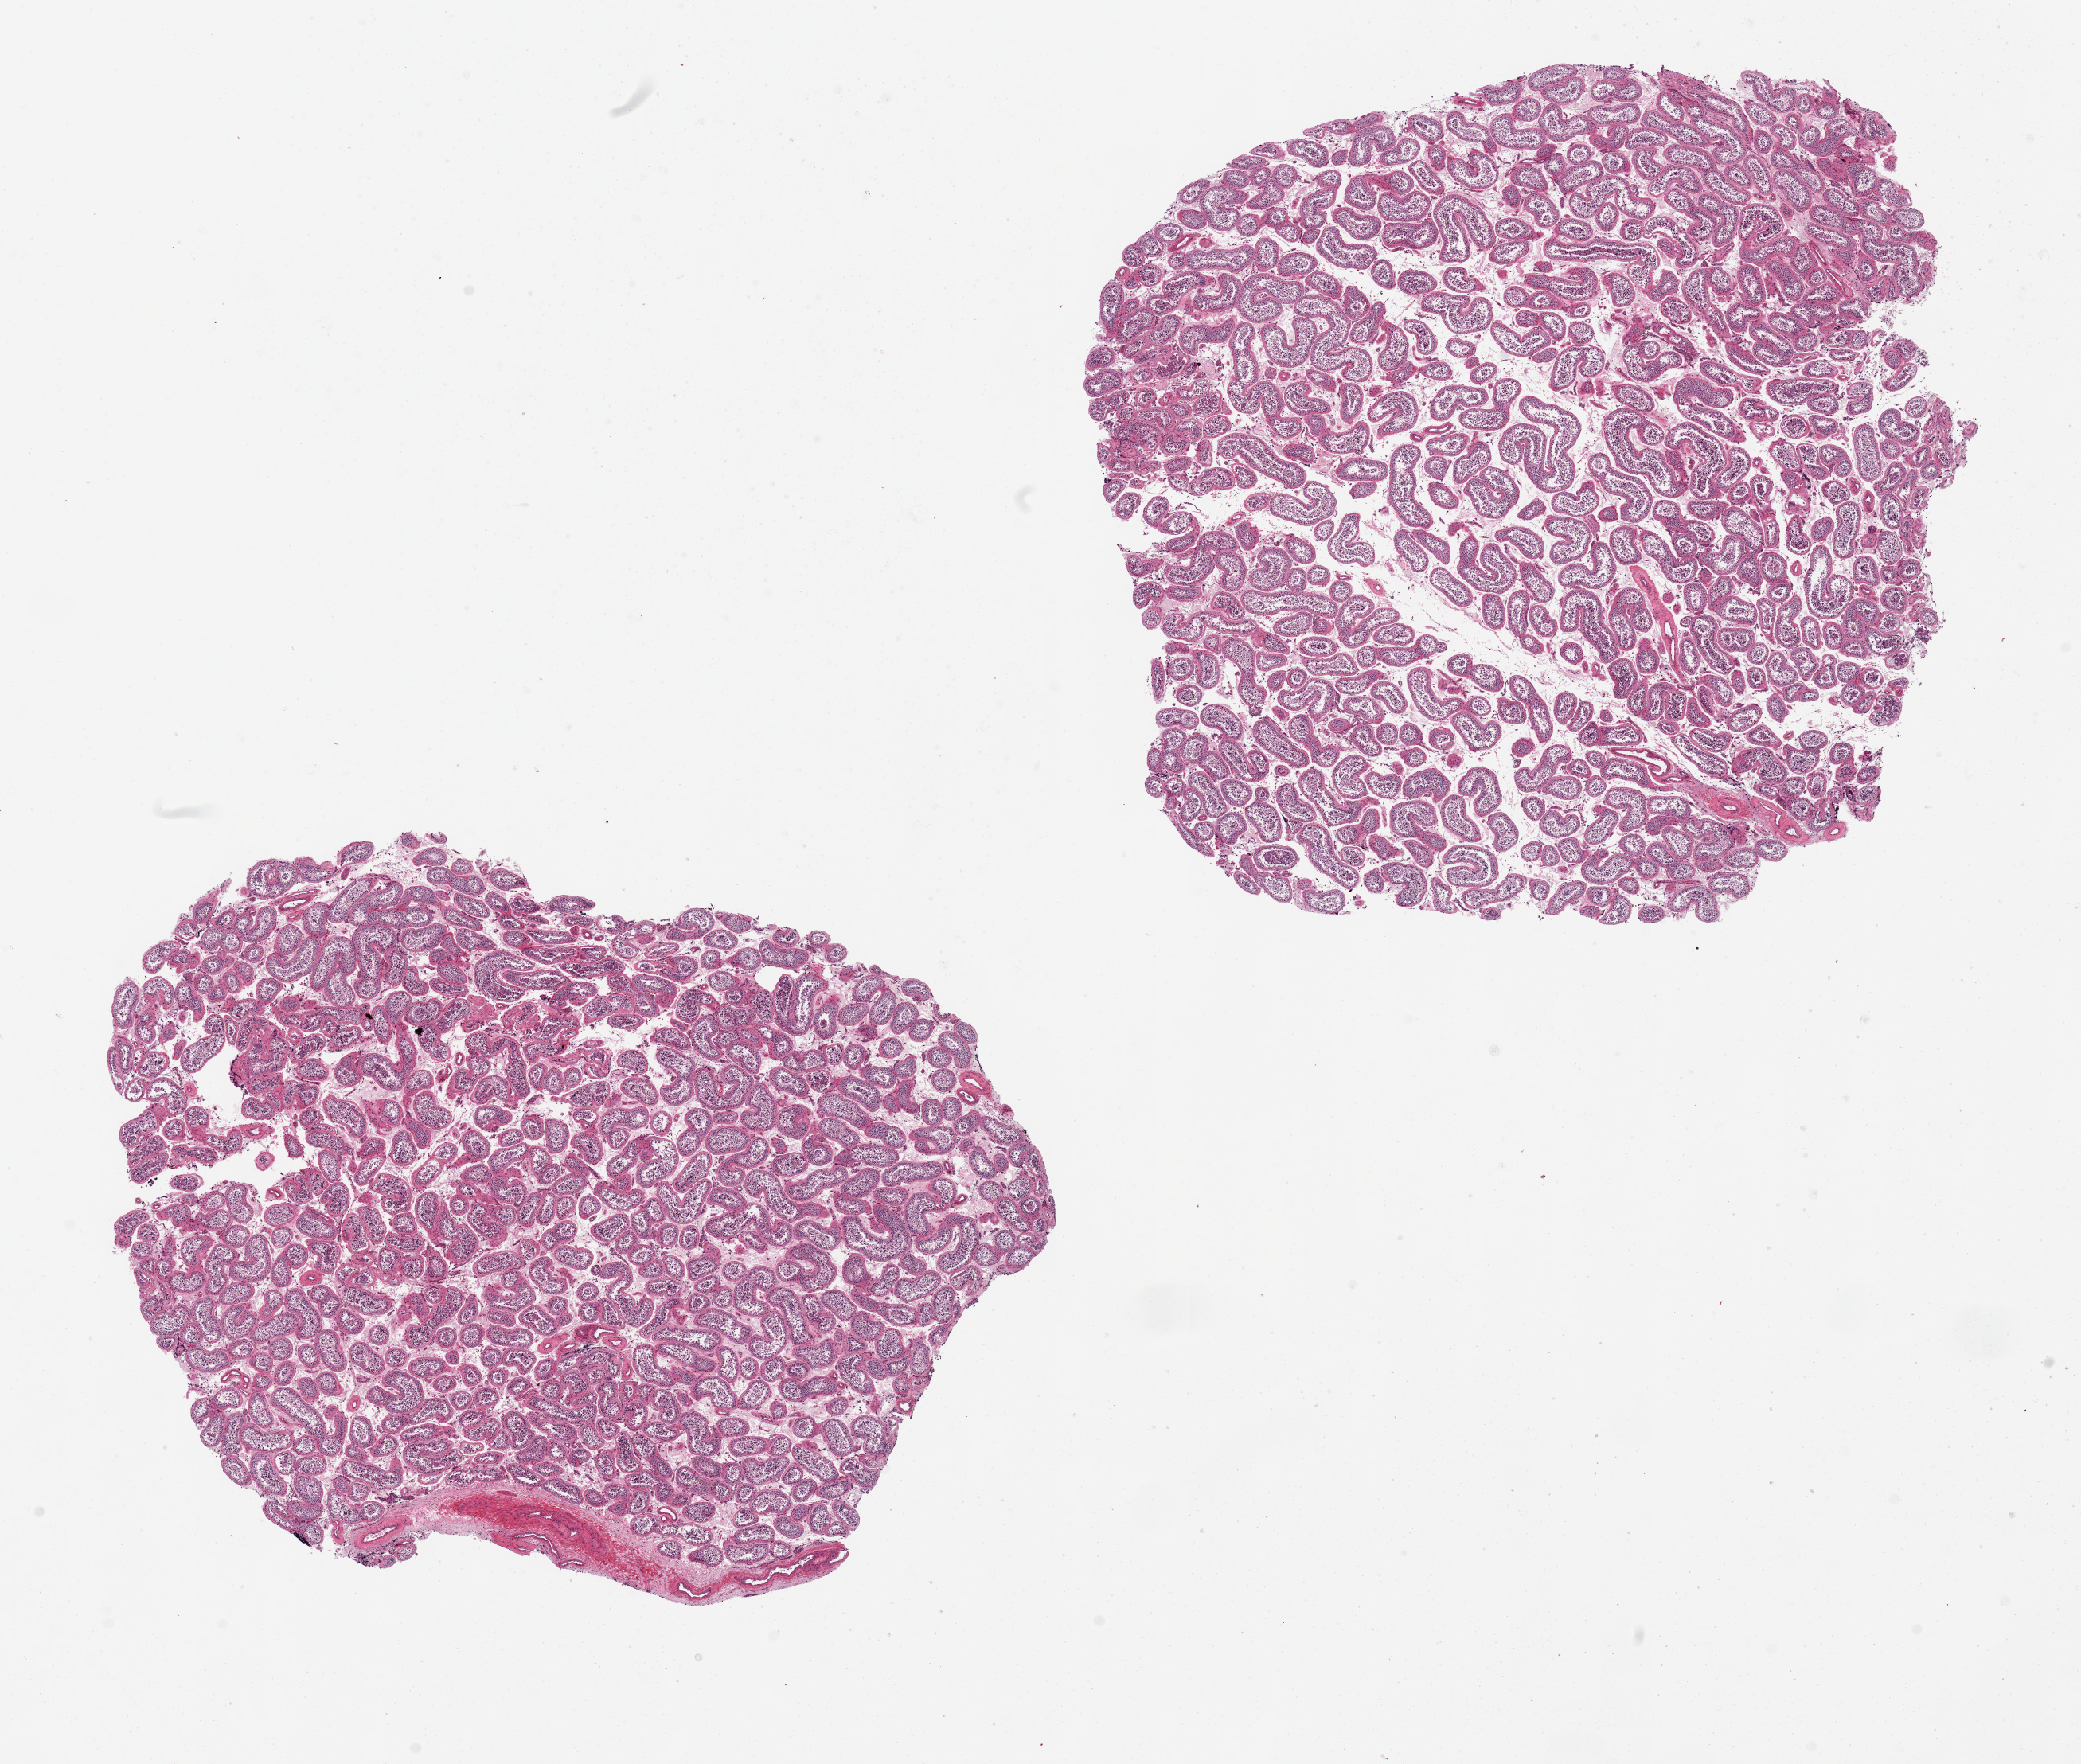
Hematoxylin and eosin (H&E) whole-slide image — whole scanned area (about 20.7 x 17.5 mm) shown as a low-resolution overview; PAXgene-fixed, paraffin-embedded tissue; sampled site (target tissue): testis; tissue donor sample. Male donor.
• pathologist's review note for this sample: 2 pieces, 10x7 & 9x8mm; spermatogenesis